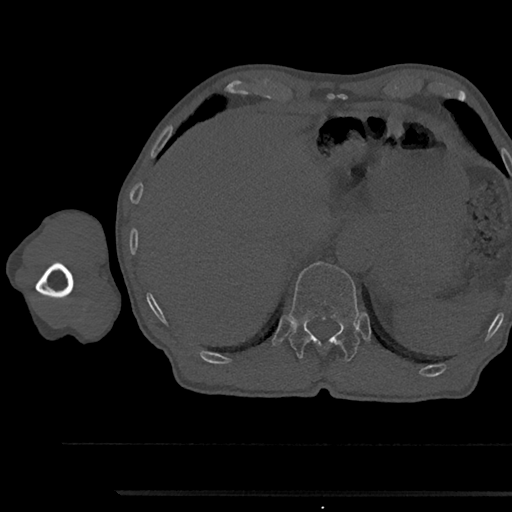
CT including the spine, one axial slice; position 727 of 797 along the scan axis; 120 kVp; bone window (W 1800 / L 400 HU); 0.5 mm slice thickness; 512 × 512 image matrix, field of view 367 × 367 mm. Male patient, age 79 years. From the clinical record (not read from this slice): primary cancer: prostate.
Structures marked on this image (semi-automatic segmentation, software-assisted and operator-edited):
- T12 vertebra: bounding box (x1, y1, x2, y2) in pixels: (289, 261, 360, 361)